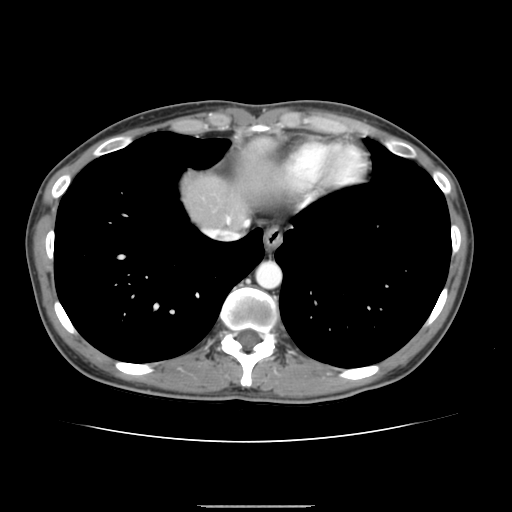
Contrast-enhanced abdominal CT, one axial slice; position 135 of 150 along the scan axis; 120 kVp; intravenous contrast given; soft-tissue window (W 400 / L 40 HU); 2.5 mm slice thickness; 512 × 512 image matrix. Female patient, age 32 years. From the clinical record (not read from this slice): diagnosis: colorectal cancer liver metastases, imaged before liver resection; multiple liver metastases: yes; largest metastasis: 0.7 cm.
Outlined on this slice (outlined manually by an expert reader):
- hepatic veins: box from (x=206, y=221) to (x=248, y=239) px
- liver: (x=184, y=178)–(x=245, y=228)
- planned liver remnant (the part of the liver to remain after resection): (x=184, y=177)–(x=244, y=229)
- portal vein (with intrahepatic branches): (x=226, y=217)–(x=230, y=222)